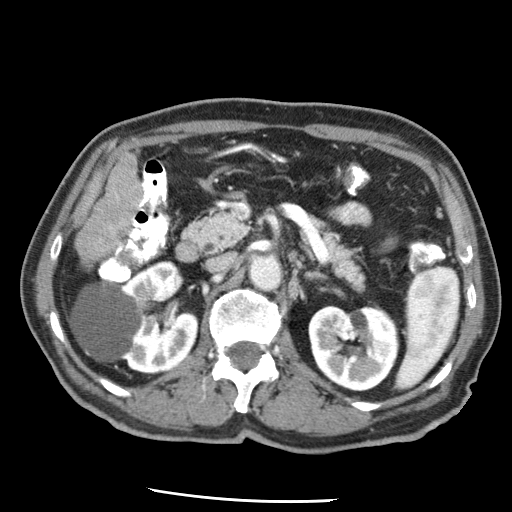
Contrast-enhanced abdominal CT (liver protocol), one axial slice. Reconstruction kernel STANDARD. 120 kVp. Soft-tissue window (W 400 / L 40 HU). 2.5 mm slice thickness. 512 × 512 image matrix, field of view 320 × 320 mm. From the clinical record (not read from this slice): diagnosis: hepatocellular carcinoma (patient treated with transarterial chemoembolisation; whether this scan precedes or follows treatment is not stated here); TNM stage (as recorded): Stage-IIIA; Child-Pugh class: A; tumour differentiation: moderately differentiated; tumour nodularity: multinodular.
Structures marked on this image (semi-automatically segmented with operator editing):
- liver parenchyma outside the tumour (the mass and vessels are separate outlines, so this box may not span the whole liver): box from (x=96, y=153) to (x=140, y=218) px